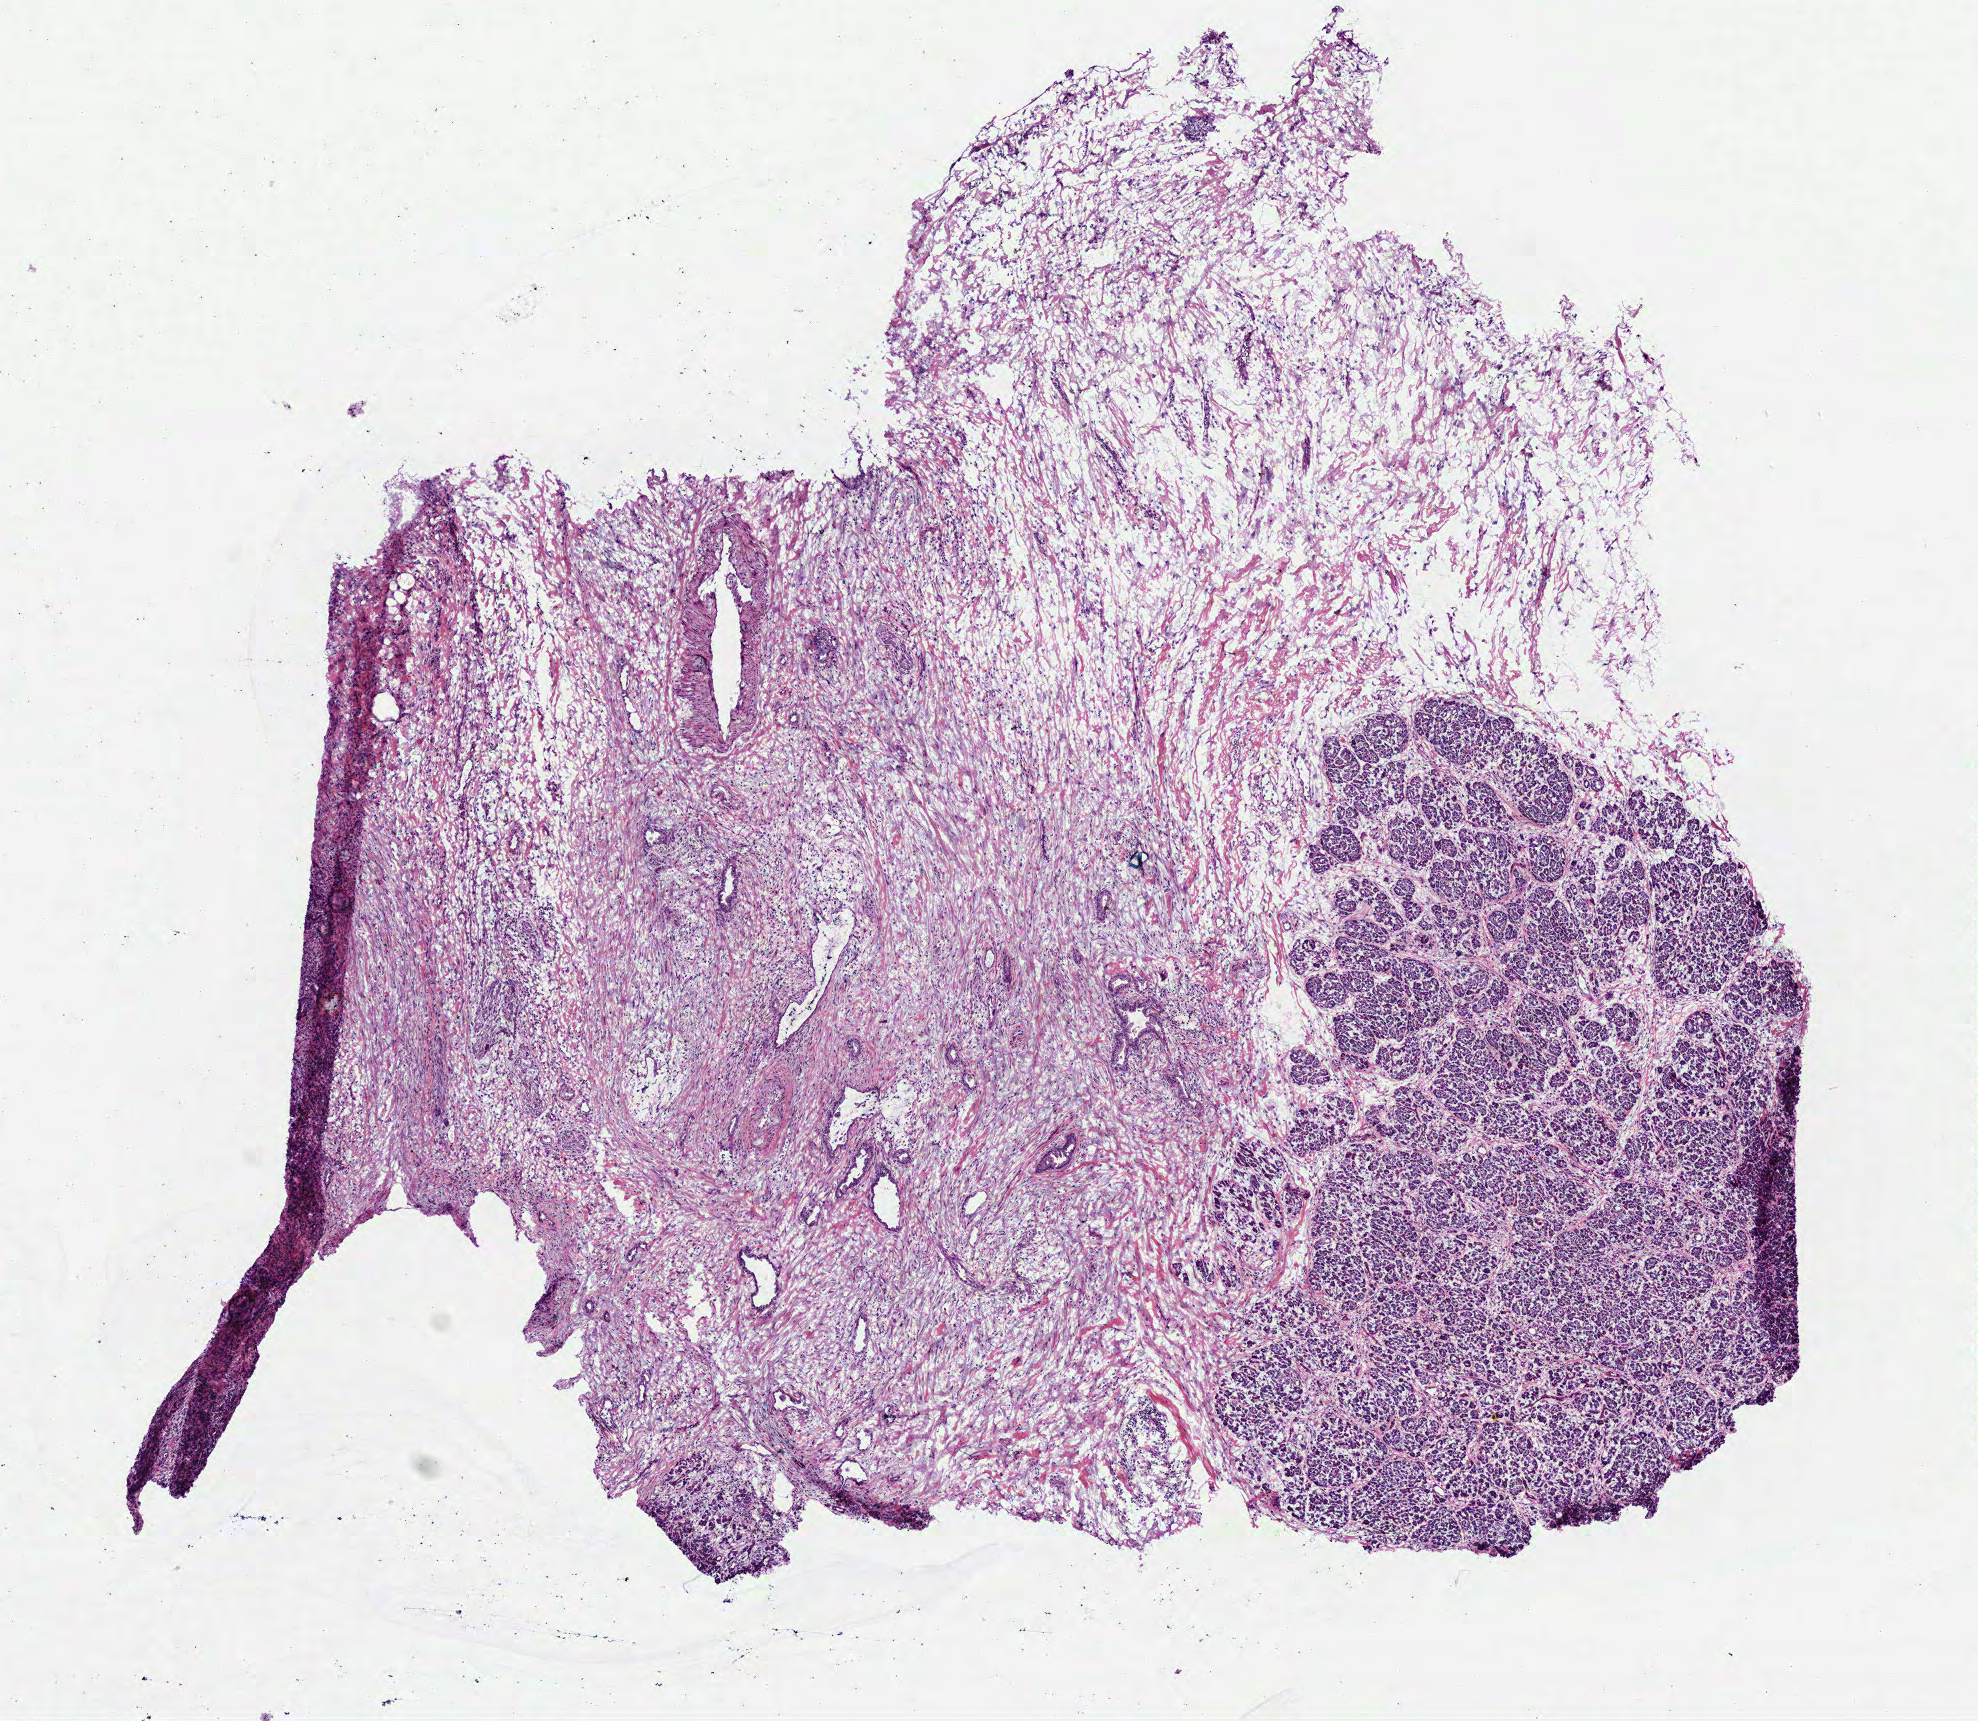
Digitized H&E tissue section (whole slide) — low-resolution overview of the scanned area, about 8.0 x 6.9 mm, frozen section from the top of the tissue portion, pancreas, primary tumour sample. Patient: female, age at initial diagnosis 69 years. Histologic grade: G1 (well differentiated). Slide review estimates, as recorded: tumour cells 32%, tumour nuclei 10%, normal cells 26%, stromal cells 42%, necrosis 0%. Inflammatory infiltration, as recorded: lymphocyte infiltration 2%, monocyte infiltration 0%, neutrophil infiltration 1%.
- AJCC pathologic stage: IIB (7th edition)
- lymph nodes positive (case pathology): 4 of 13 examined
- pathologic diagnosis: Infiltrating duct carcinoma, NOS (head of pancreas)